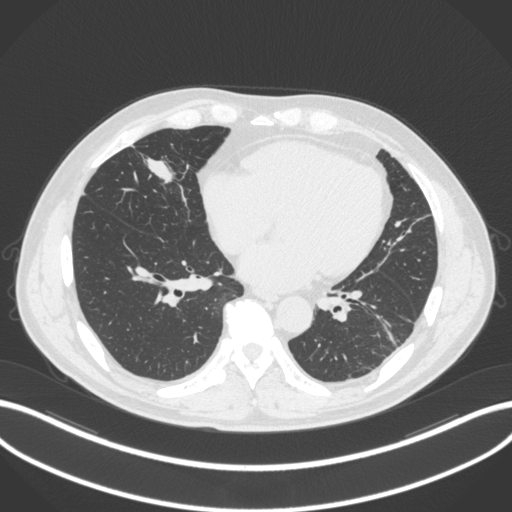
Chest CT, one axial slice. Position 102 of 399 along the scan axis. Reconstruction kernel B31f. Lung window (W 1500 / L -600 HU). 1 mm slice thickness. 512 × 512 image matrix, field of view 400 × 400 mm. Patient: male, 59 years. From the clinical record (not read from this slice): clinical TNM (as recorded): T2a N1 M0.
Annotated regions visible in this slice (bounding box drawn by a radiologist):
- lung tumour (recorded histology: adenocarcinoma): bounding box [x1, y1, x2, y2] px = [140, 147, 189, 196]